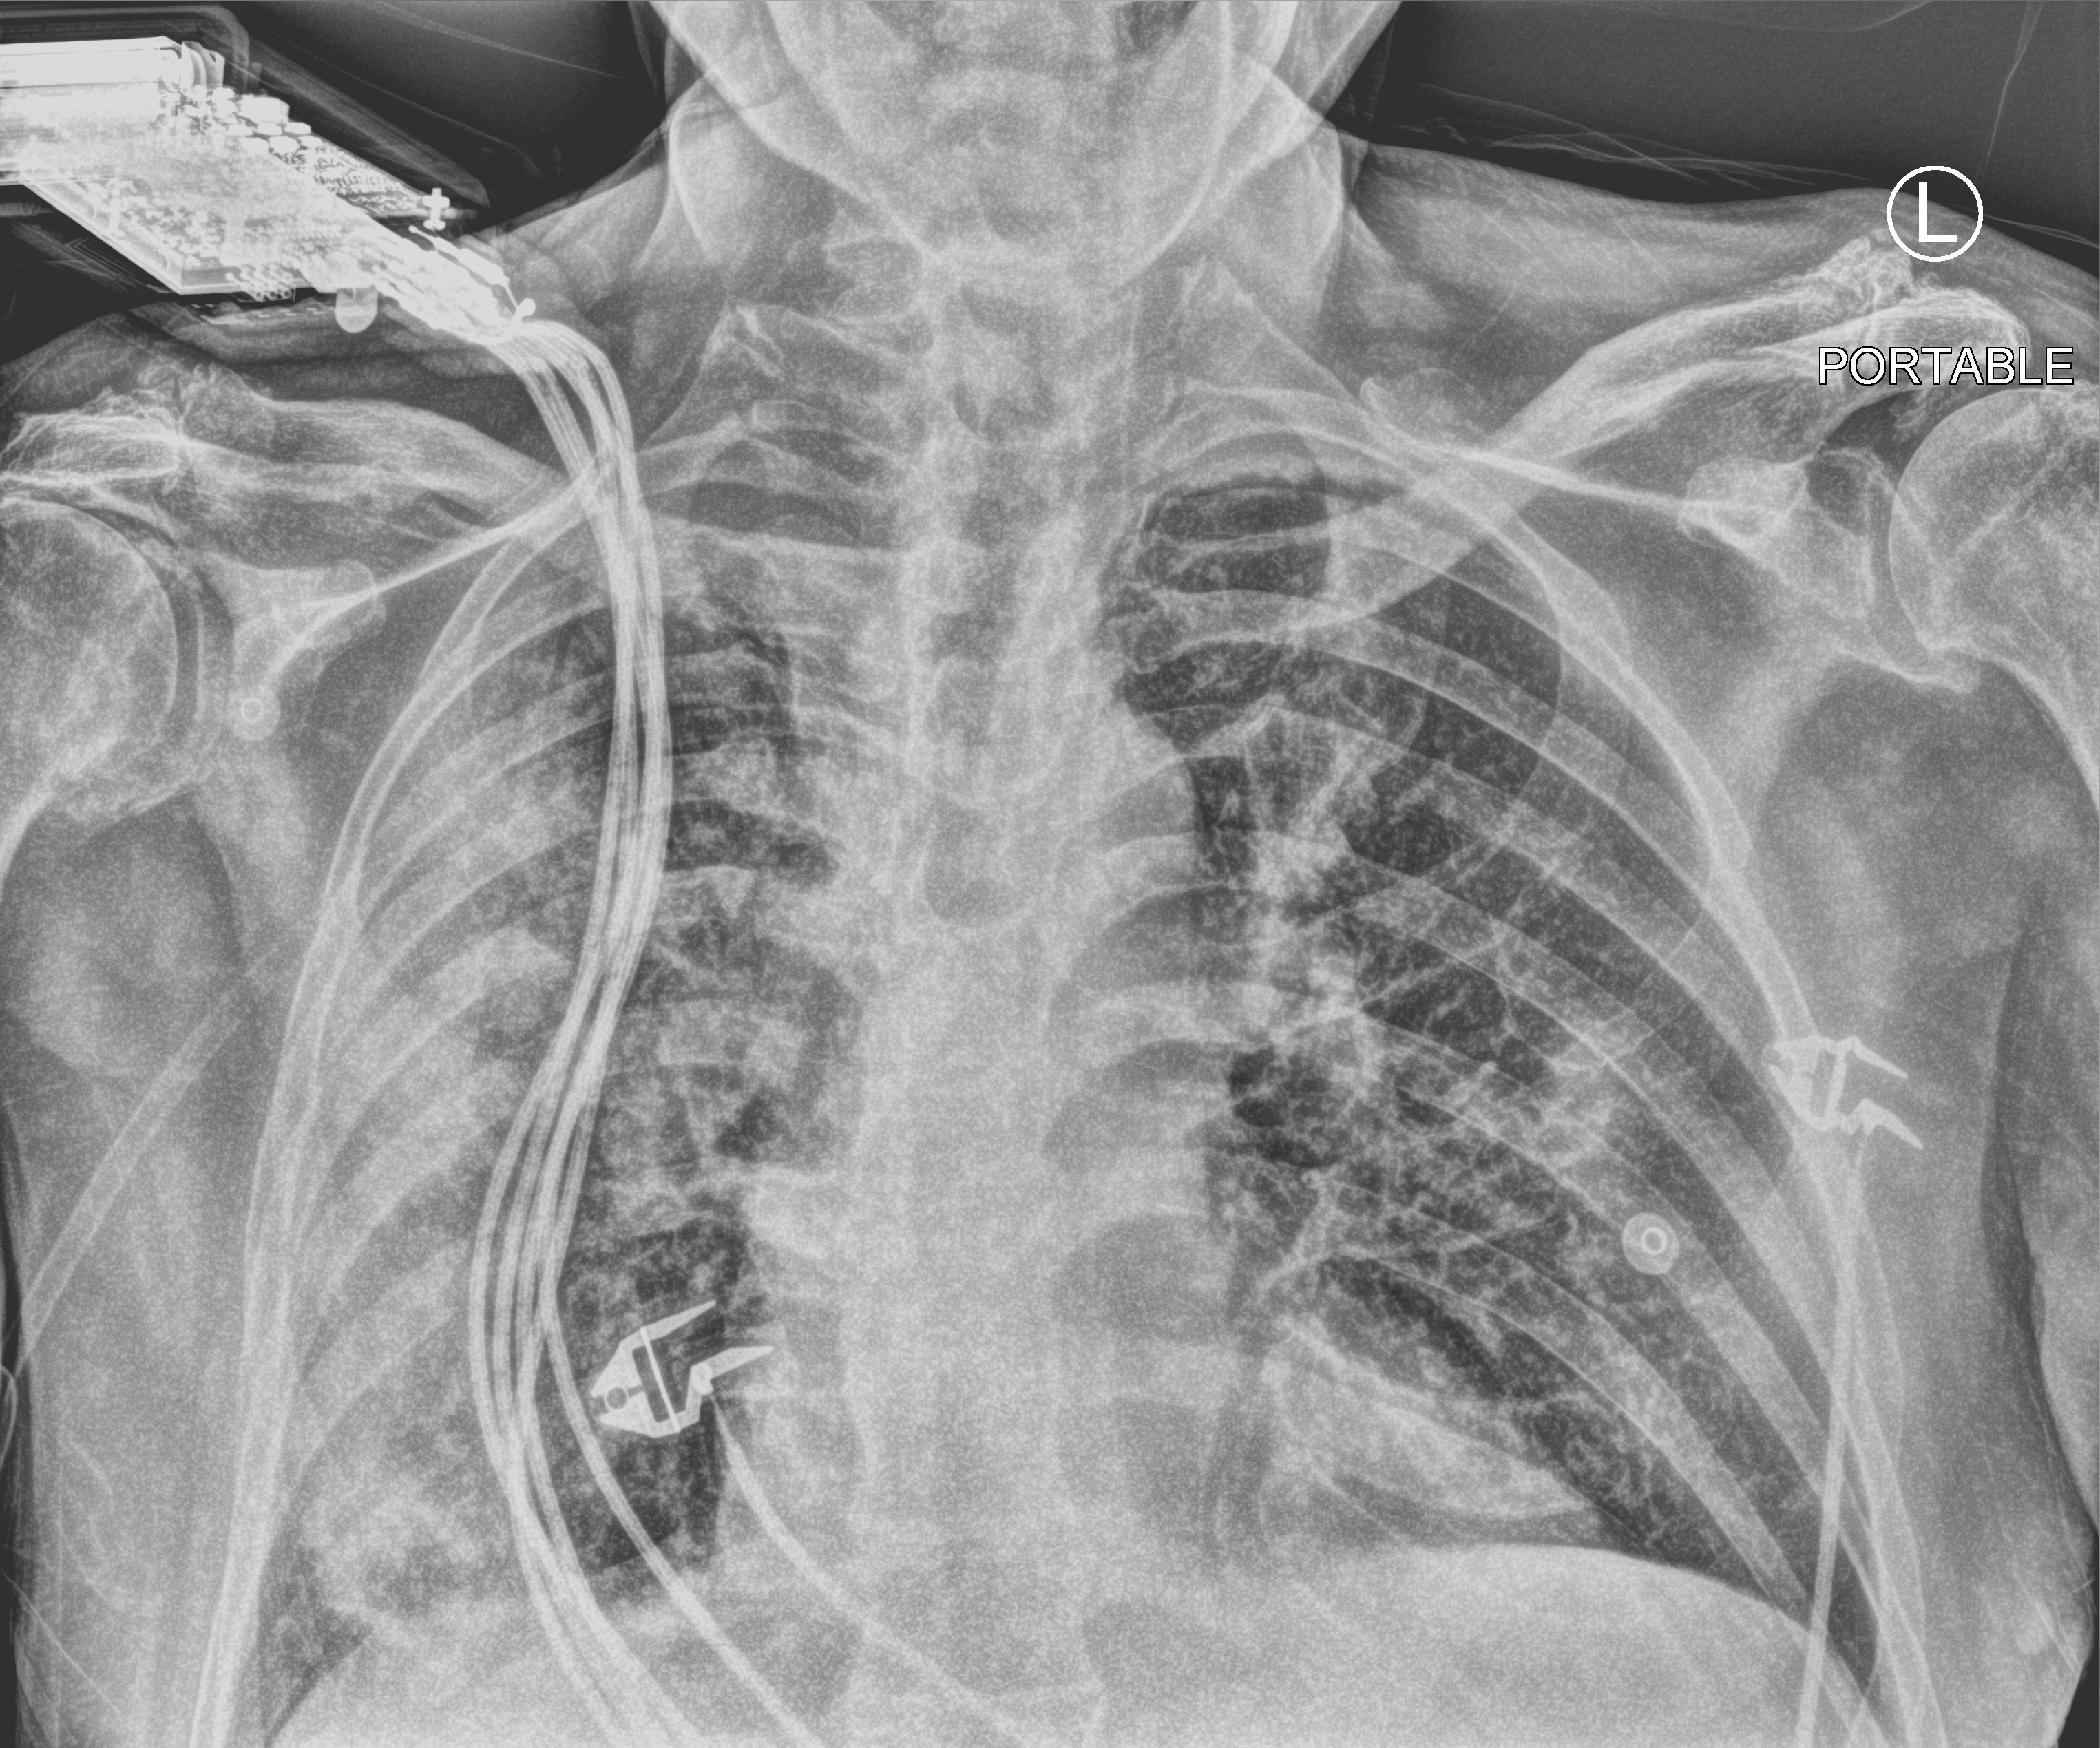
Bedside chest radiograph (computed radiography); anteroposterior (AP) projection. Male patient hospitalised with COVID-19, age 75–90 years.
From the hospital-stay record, not from the radiograph (when in the stay this image was taken is not recorded): COPD (admission record): no; admitted to intensive care during this hospital stay: no.